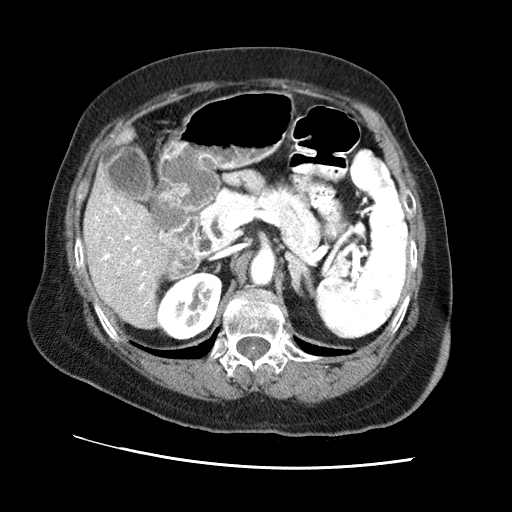
Contrast-enhanced abdominal CT (liver protocol), one axial slice. Reconstruction kernel STANDARD. Soft-tissue window (W 400 / L 40 HU). 512 × 512 image matrix. From the clinical record (not read from this slice): diagnosis: hepatocellular carcinoma (patient treated with transarterial chemoembolisation; whether this scan precedes or follows treatment is not stated here); TNM stage (as recorded): Stage-II; Child-Pugh class: A; tumour differentiation: no biopsy; tumour nodularity: multinodular.
Outlined on this slice (semi-automatic segmentation, software-assisted and operator-edited):
- liver parenchyma outside the tumour (the mass and vessels are separate outlines, so this box may not span the whole liver): bounding box [x1, y1, x2, y2] px = [84, 146, 168, 328]
- liver vessels: [95, 195, 150, 306]